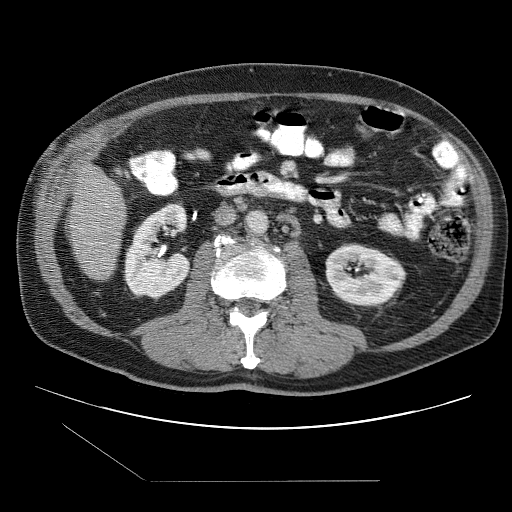
Contrast-enhanced abdominal CT (liver protocol), one axial slice; position 21 of 109 along the scan axis; reconstruction kernel STANDARD; 120 kVp; one of 2 acquisitions stored at this slice position; soft-tissue window (W 400 / L 40 HU); 2.5 mm slice thickness; 512 × 512 image matrix, field of view 400 × 400 mm. Case-level facts recorded for this patient, not image findings: diagnosis: hepatocellular carcinoma (patient treated with transarterial chemoembolisation; whether this scan precedes or follows treatment is not stated here); TNM stage (as recorded): Stage-IIIB; Child-Pugh class: A; tumour differentiation: well differentiated; tumour nodularity: multinodular.
Structures marked on this image (semi-automatically segmented with operator editing):
- liver parenchyma outside the tumour (the mass and vessels are separate outlines, so this box may not span the whole liver): box from (x=68, y=166) to (x=126, y=278) px
- liver vessels: (x=106, y=205)–(x=109, y=207)